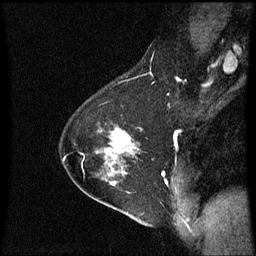
Breast MRI (dynamic contrast-enhanced), one sagittal slice; slice 42 of 60 in the series (ordered by position); dynamic contrast-enhanced series, image 2 of 3 at this slice position (ordered by acquisition); 1.5 T; TE 4.2 ms, TR 8.9 ms; 256 × 256 image matrix, field of view 200 × 200 mm. Patient: female, 54 years. From the clinical record (not read from this slice): setting: breast cancer imaged before/during neoadjuvant chemotherapy; receptor status: HER2-positive.
Outlined on this slice (semi-automatically segmented with operator editing):
- analysis volume of interest (the breast-tissue region the enhancement analysis was run in; not a lesion): box from (x=102, y=126) to (x=140, y=169) px
- tumour enhancement mask (voxels above the 70 % enhancement threshold inside the analysis volume of interest): (x=113, y=130)–(x=130, y=147)